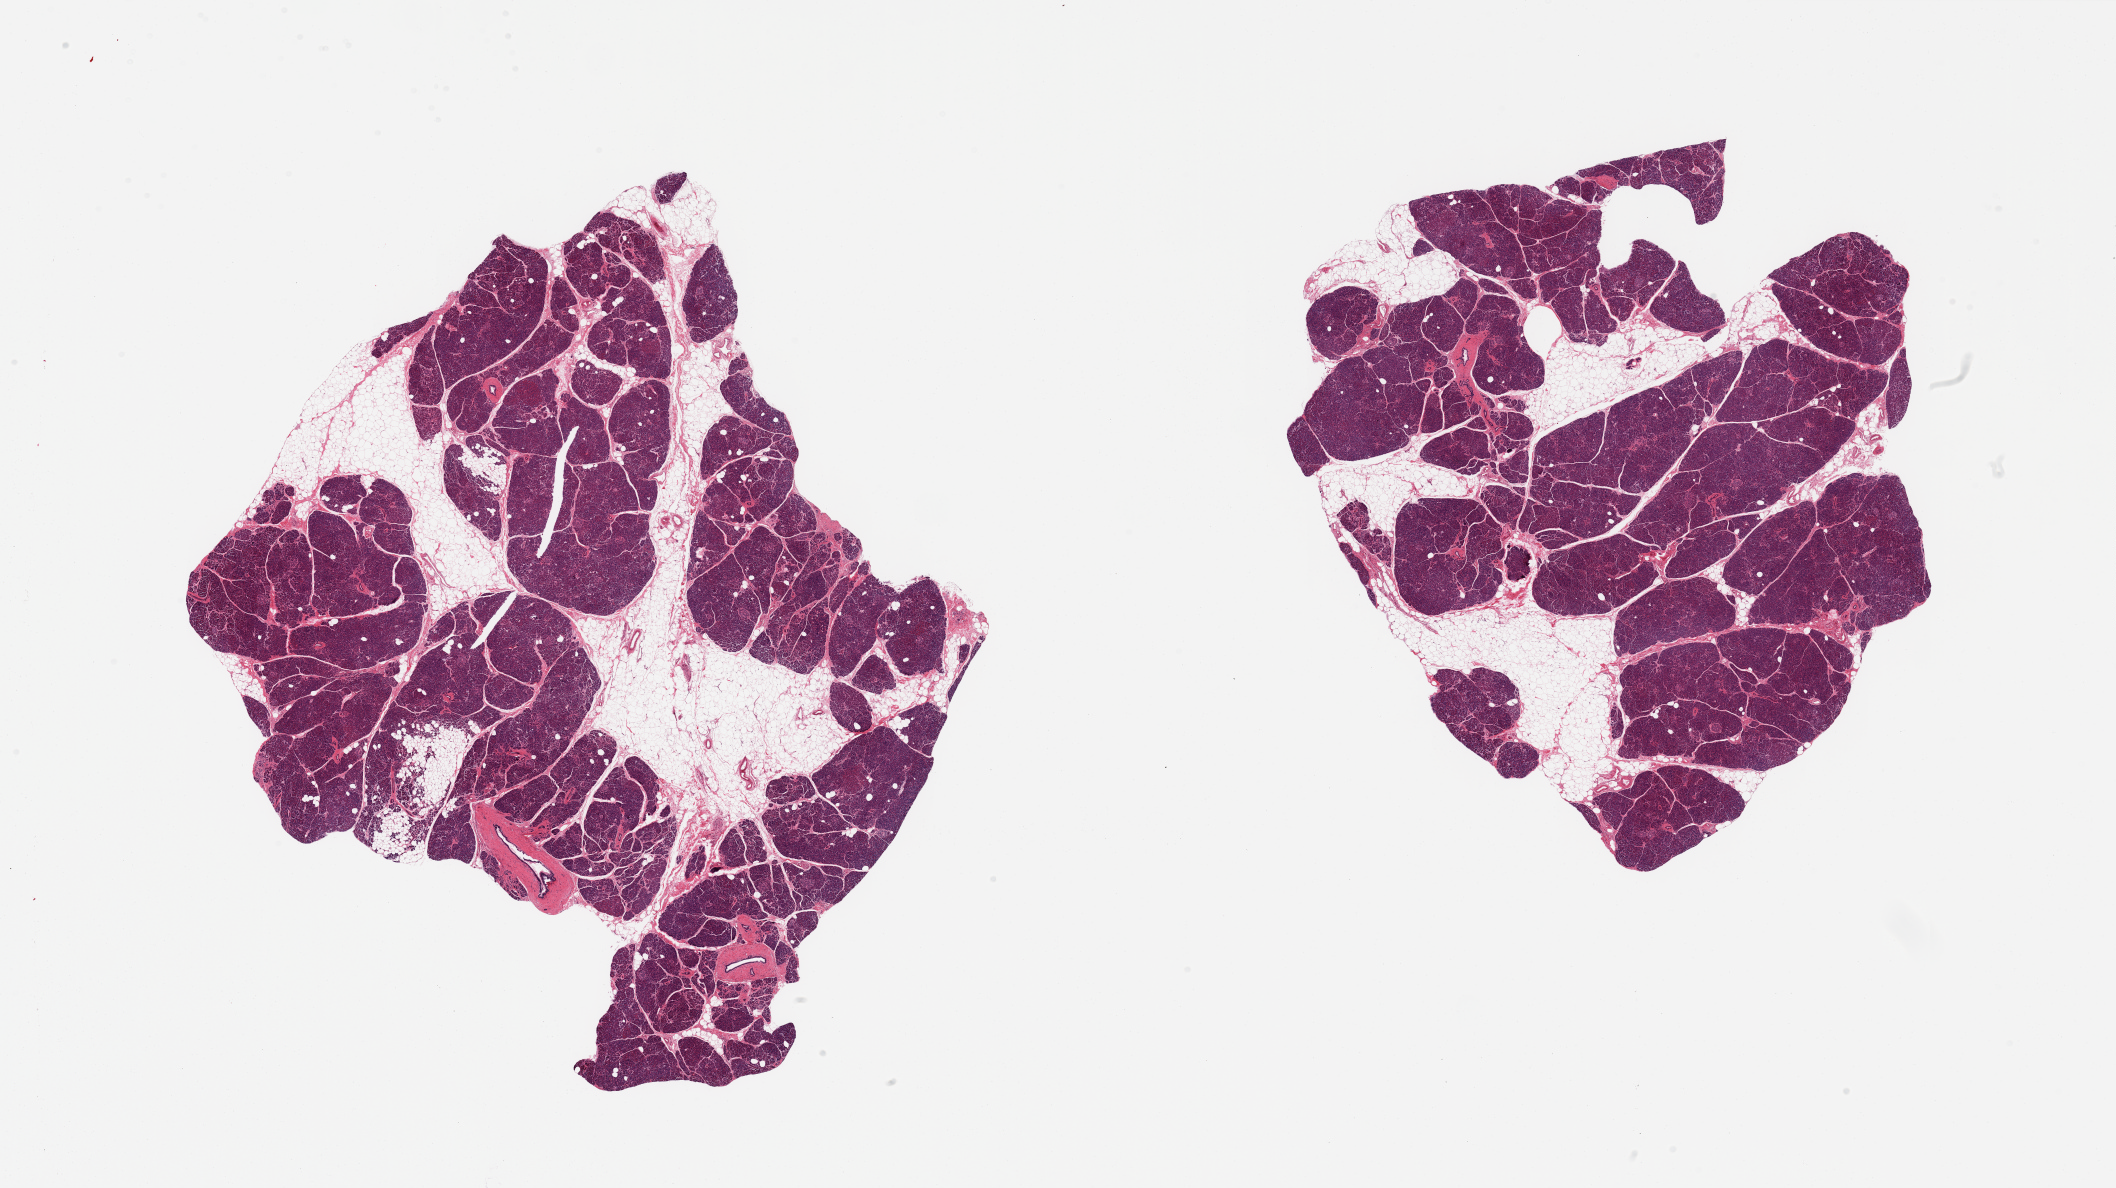
Hematoxylin and eosin (H&E) whole-slide image, brightfield — a low-resolution overview of the entire scanned area, about 33.5 x 18.8 mm (from a 20x scan), PAXgene-fixed paraffin-embedded (PFPE) section, section of pancreas (target tissue), tissue donor sample. Donor sex: male.
Reviewer comment on this tissue sample: 2 pieces; 30% internal fat.